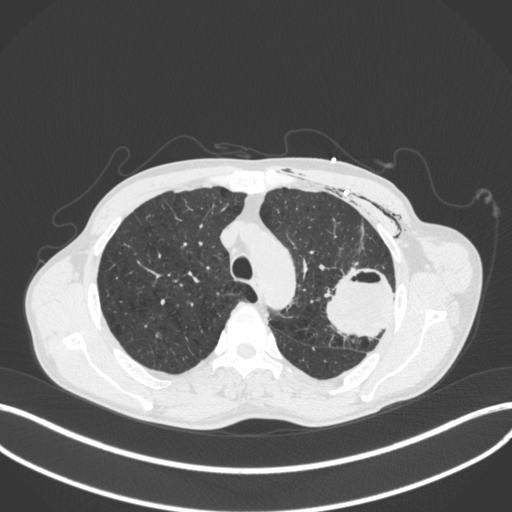
Chest CT, one axial slice; position 303 of 416 along the scan axis; lung window (W 1500 / L -600 HU); 1 mm slice thickness; 512 × 512 image matrix, field of view 400 × 400 mm. Male patient, age 58 years. From the clinical record (not read from this slice): clinical TNM (as recorded): T3 N0 M0.
Annotated regions visible in this slice (bounding box drawn by a radiologist):
- lung tumour (recorded histology: adenocarcinoma): bounding box [x1, y1, x2, y2] px = [322, 266, 401, 344]